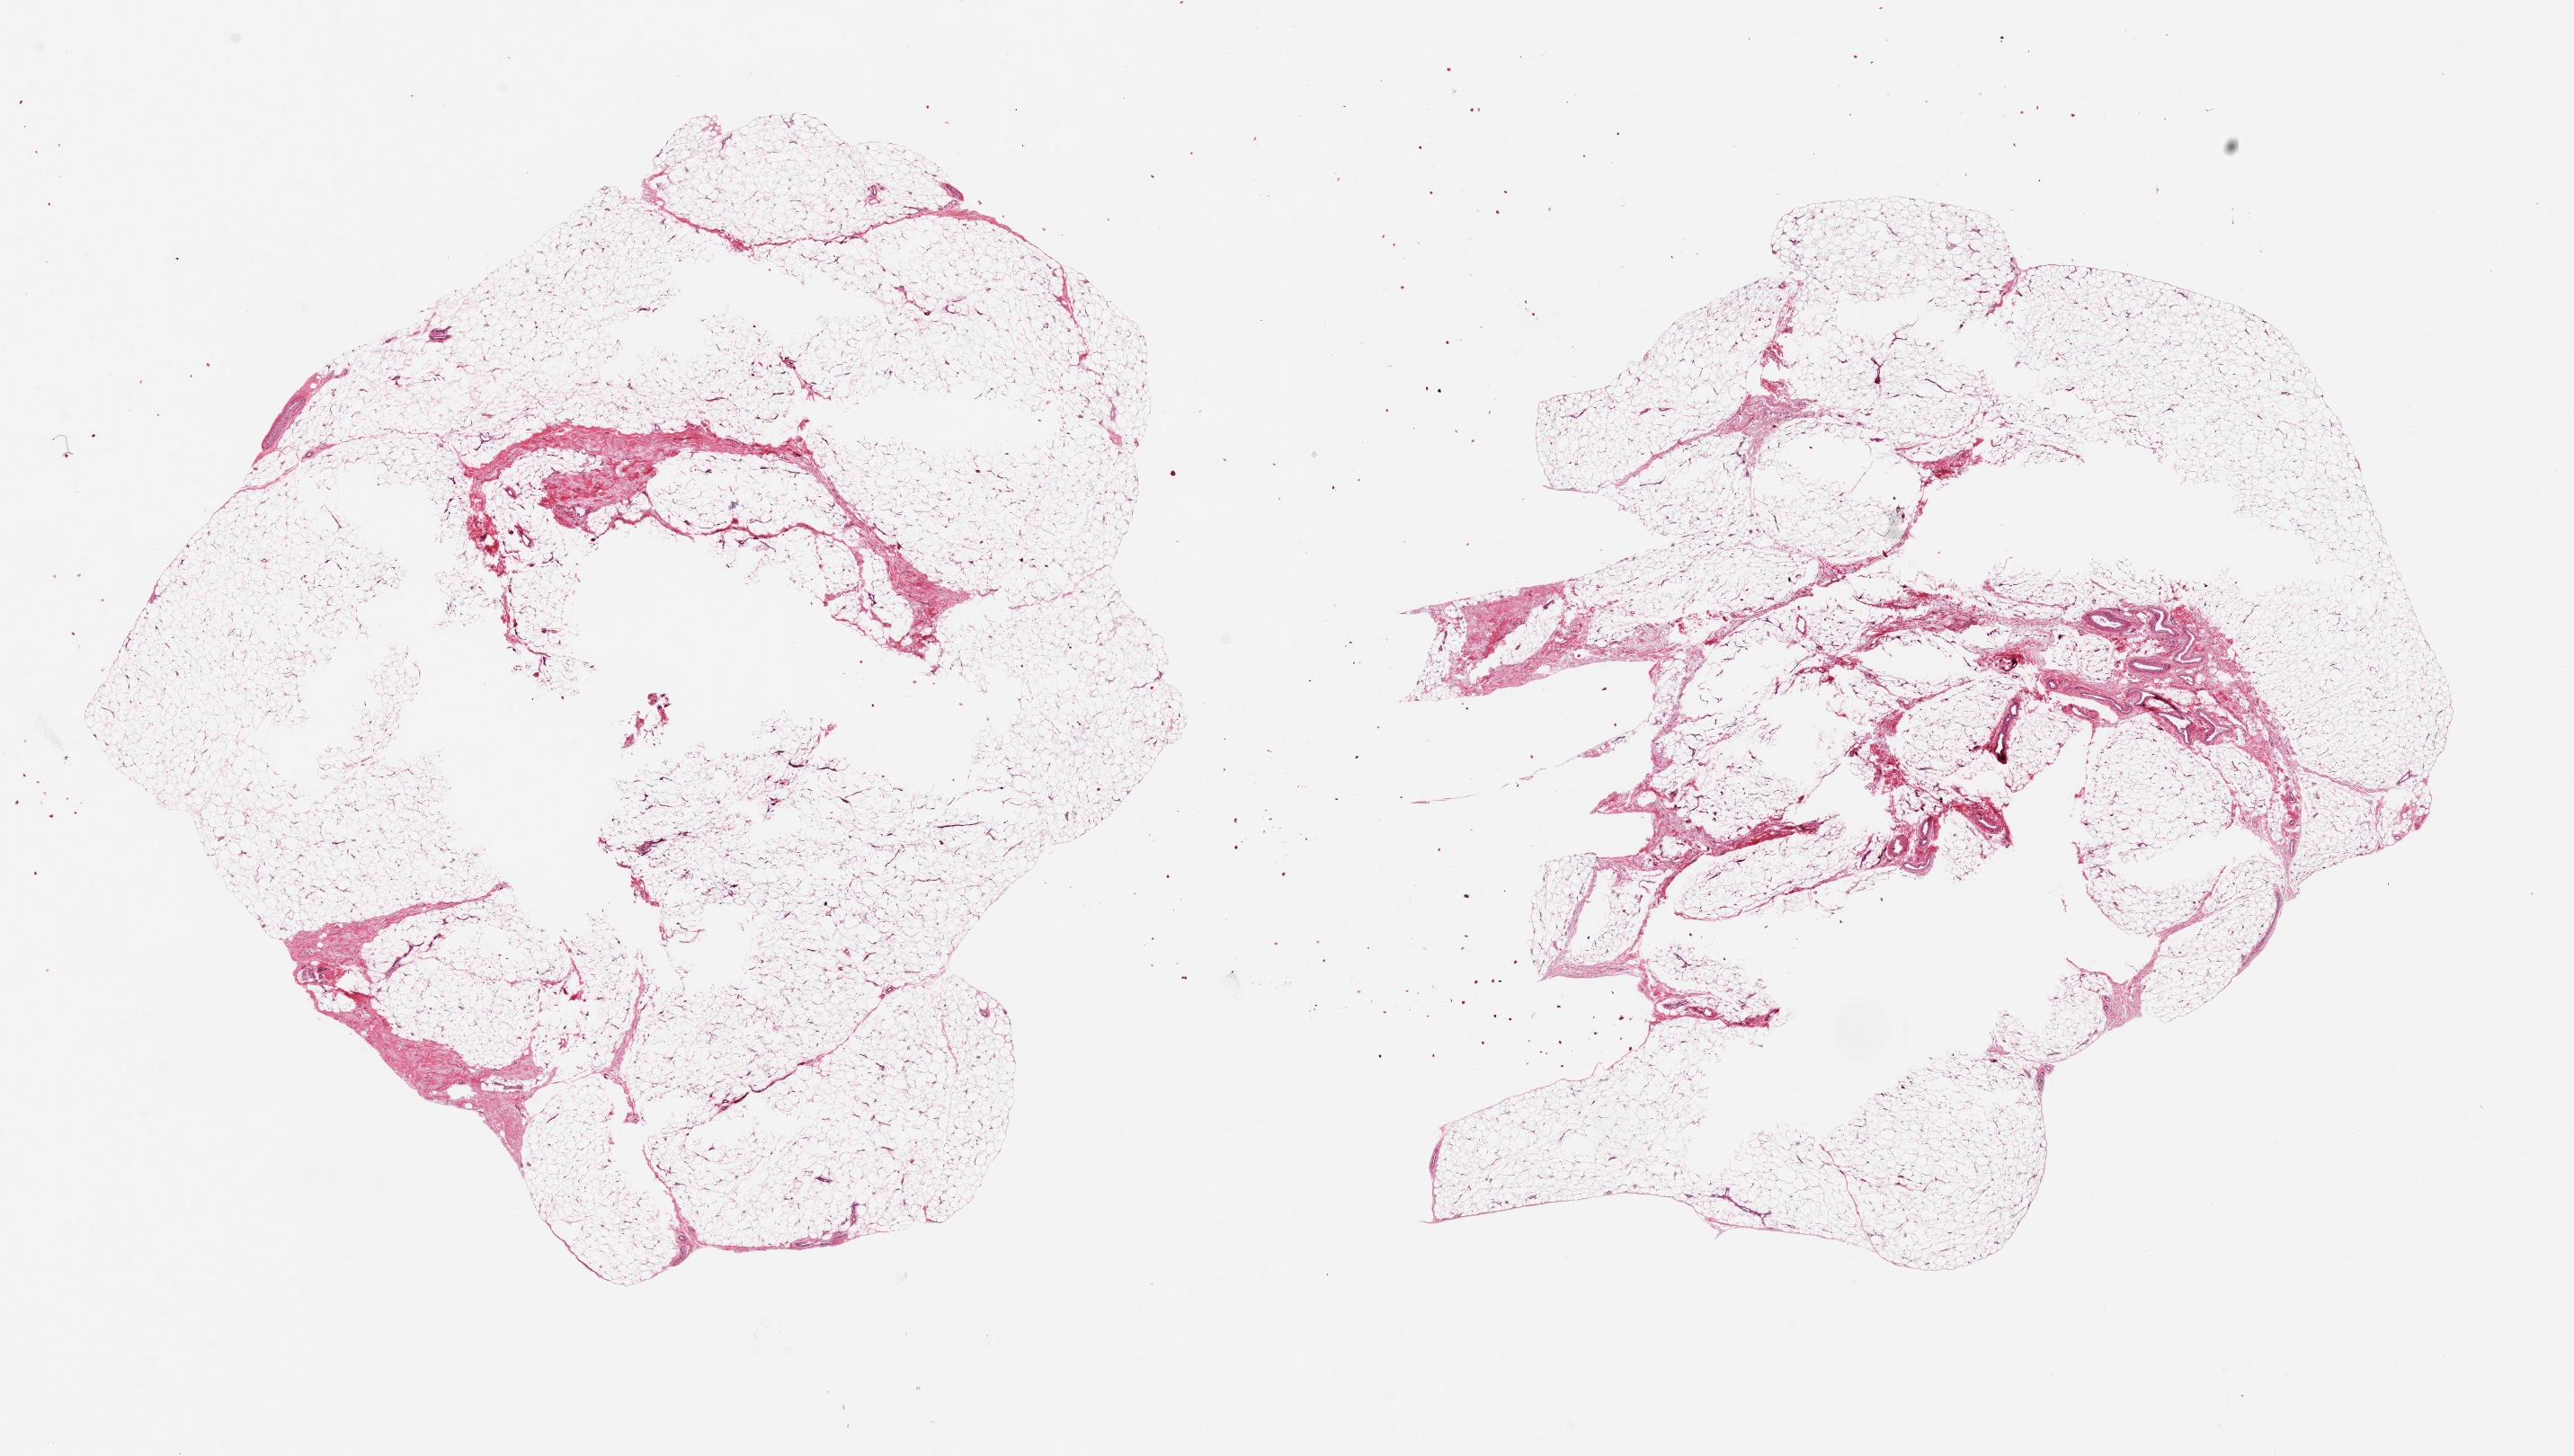
Digitized haematoxylin and eosin-stained section, brightfield, a low-resolution overview of the entire scanned area, about 22.6 x 12.8 mm (from a 20x scan), PAXgene-fixed, paraffin-embedded tissue, target tissue: adipose tissue, tissue donor sample. Donor: male.
Reviewer comment on this tissue sample: 2 ~9x9mm aliquots.